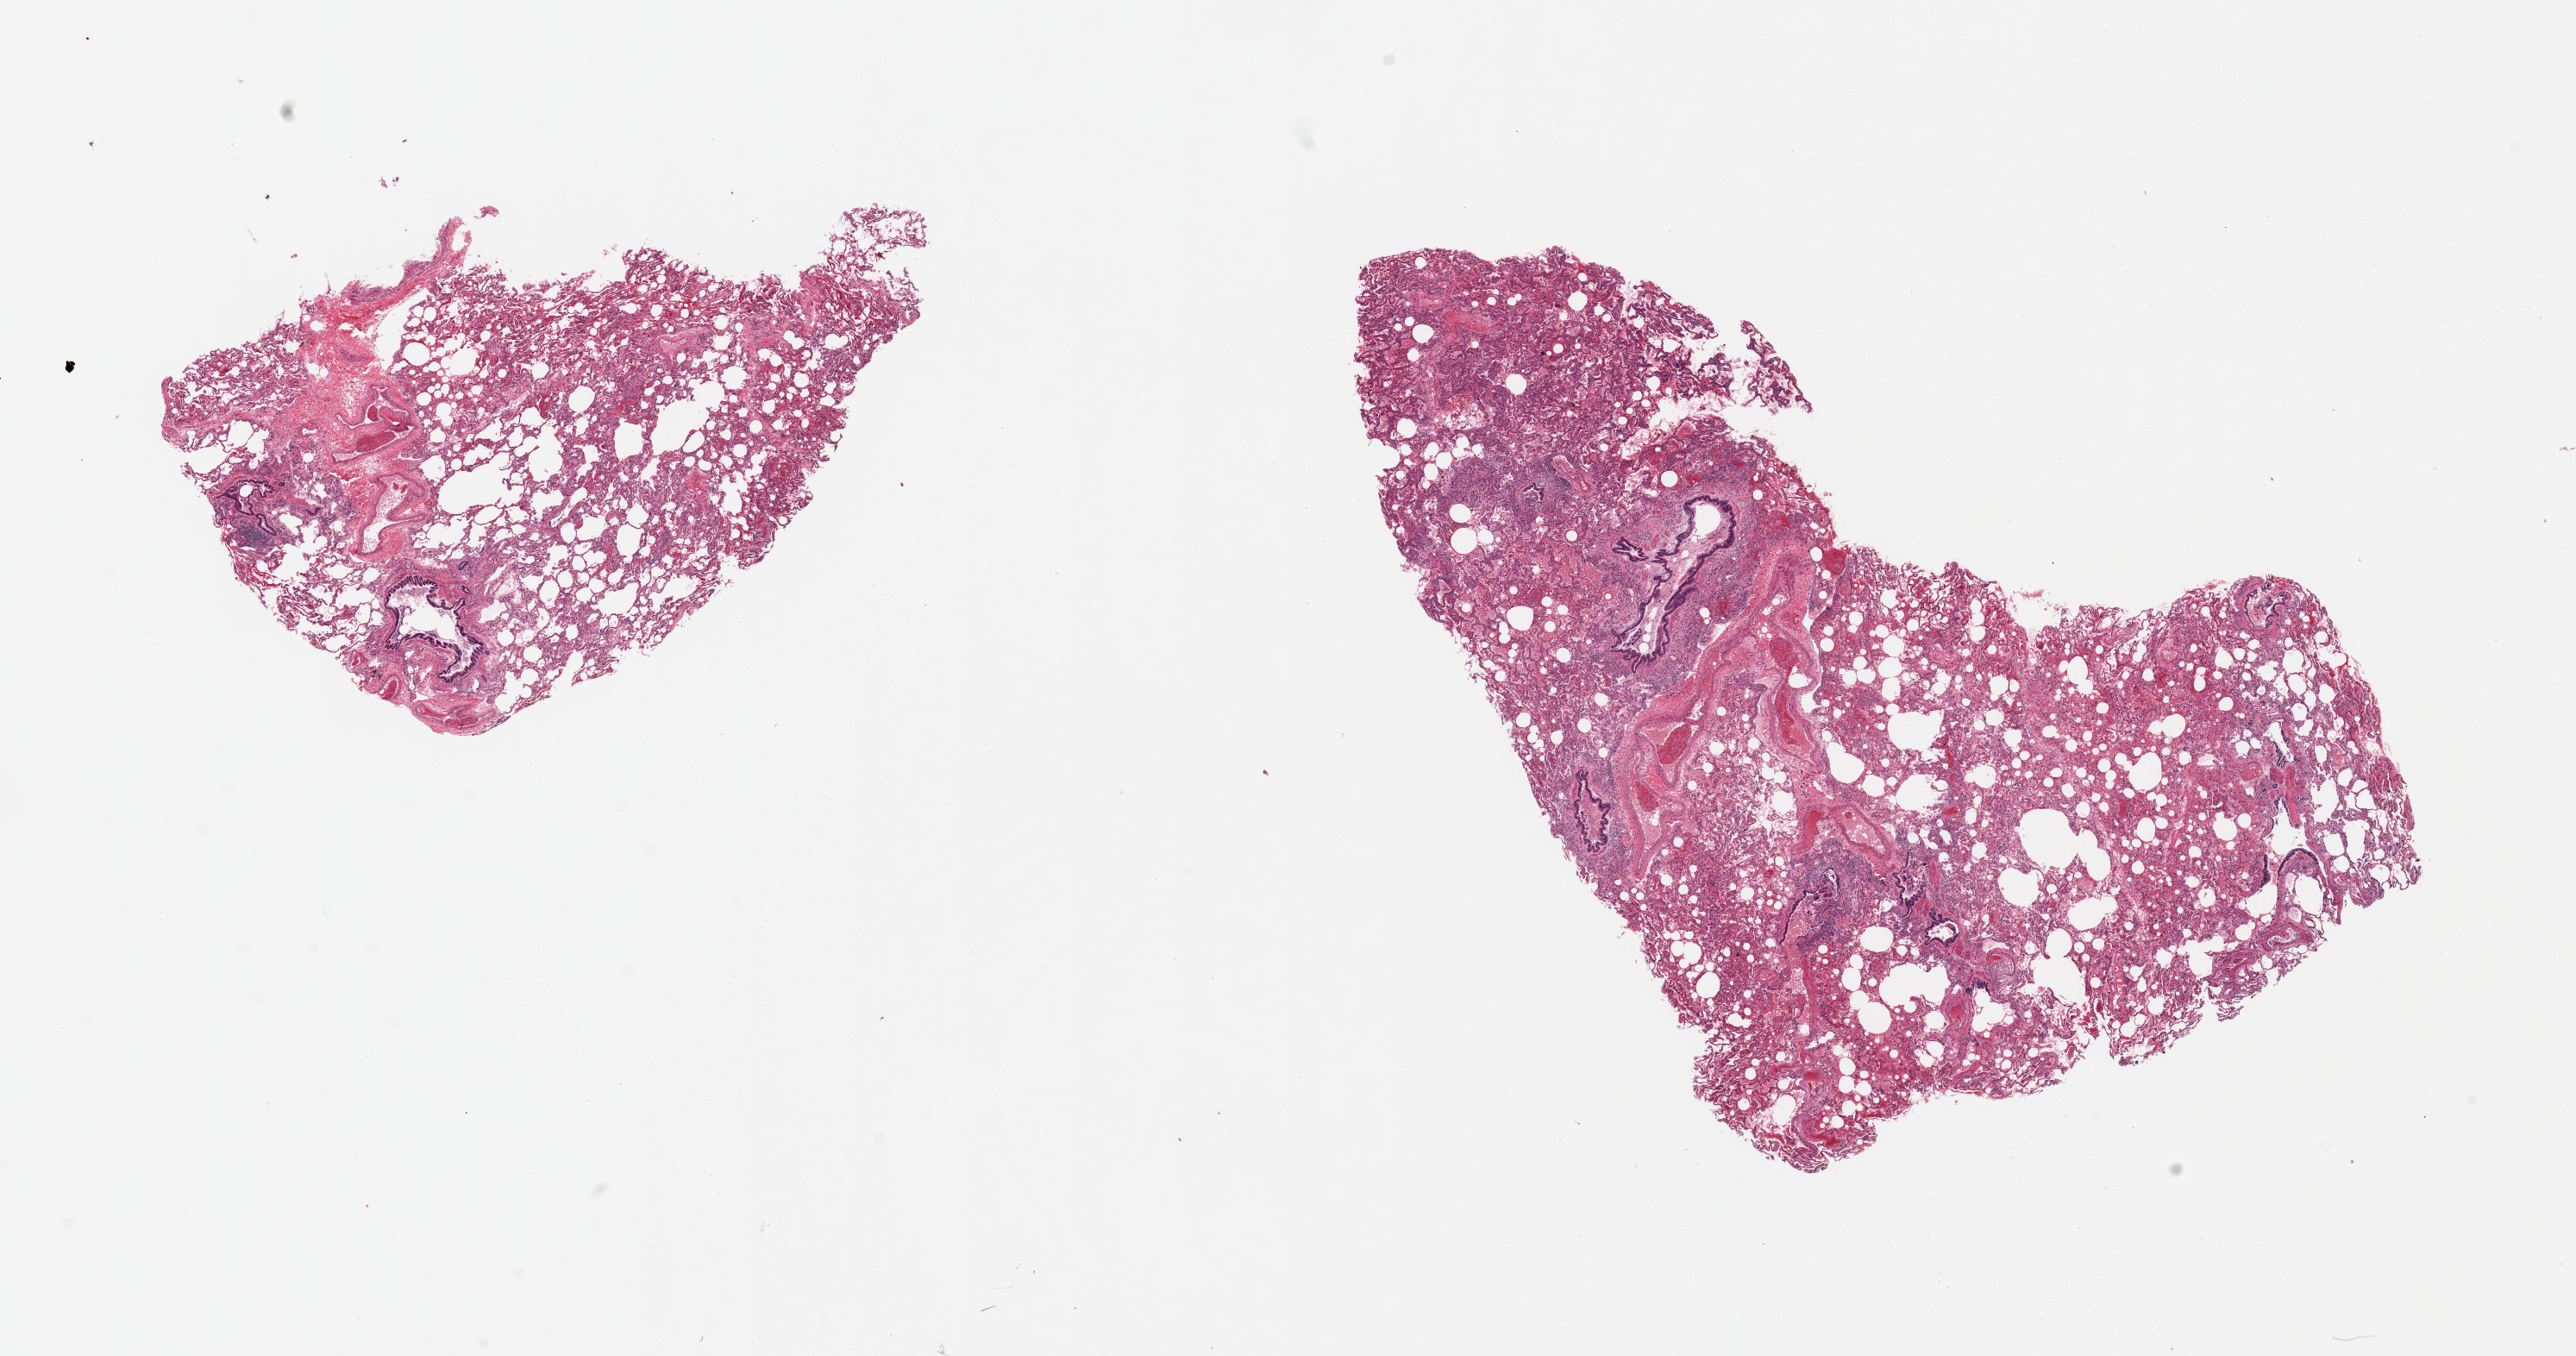
Digitized haematoxylin and eosin-stained section, shown as a low-resolution overview of the whole scanned area (about 23.6 x 12.4 mm, slide scanned at 20x); PAXgene-fixed, paraffin-embedded tissue; section of lung (target tissue); donor tissue sample. Donor sex: female.
* reviewer comment on this tissue sample: 2 pieces moderate congestion, chronic & focal acute pneumonitis, a few giant cells noted in bronchial lumina, ? aspiration features